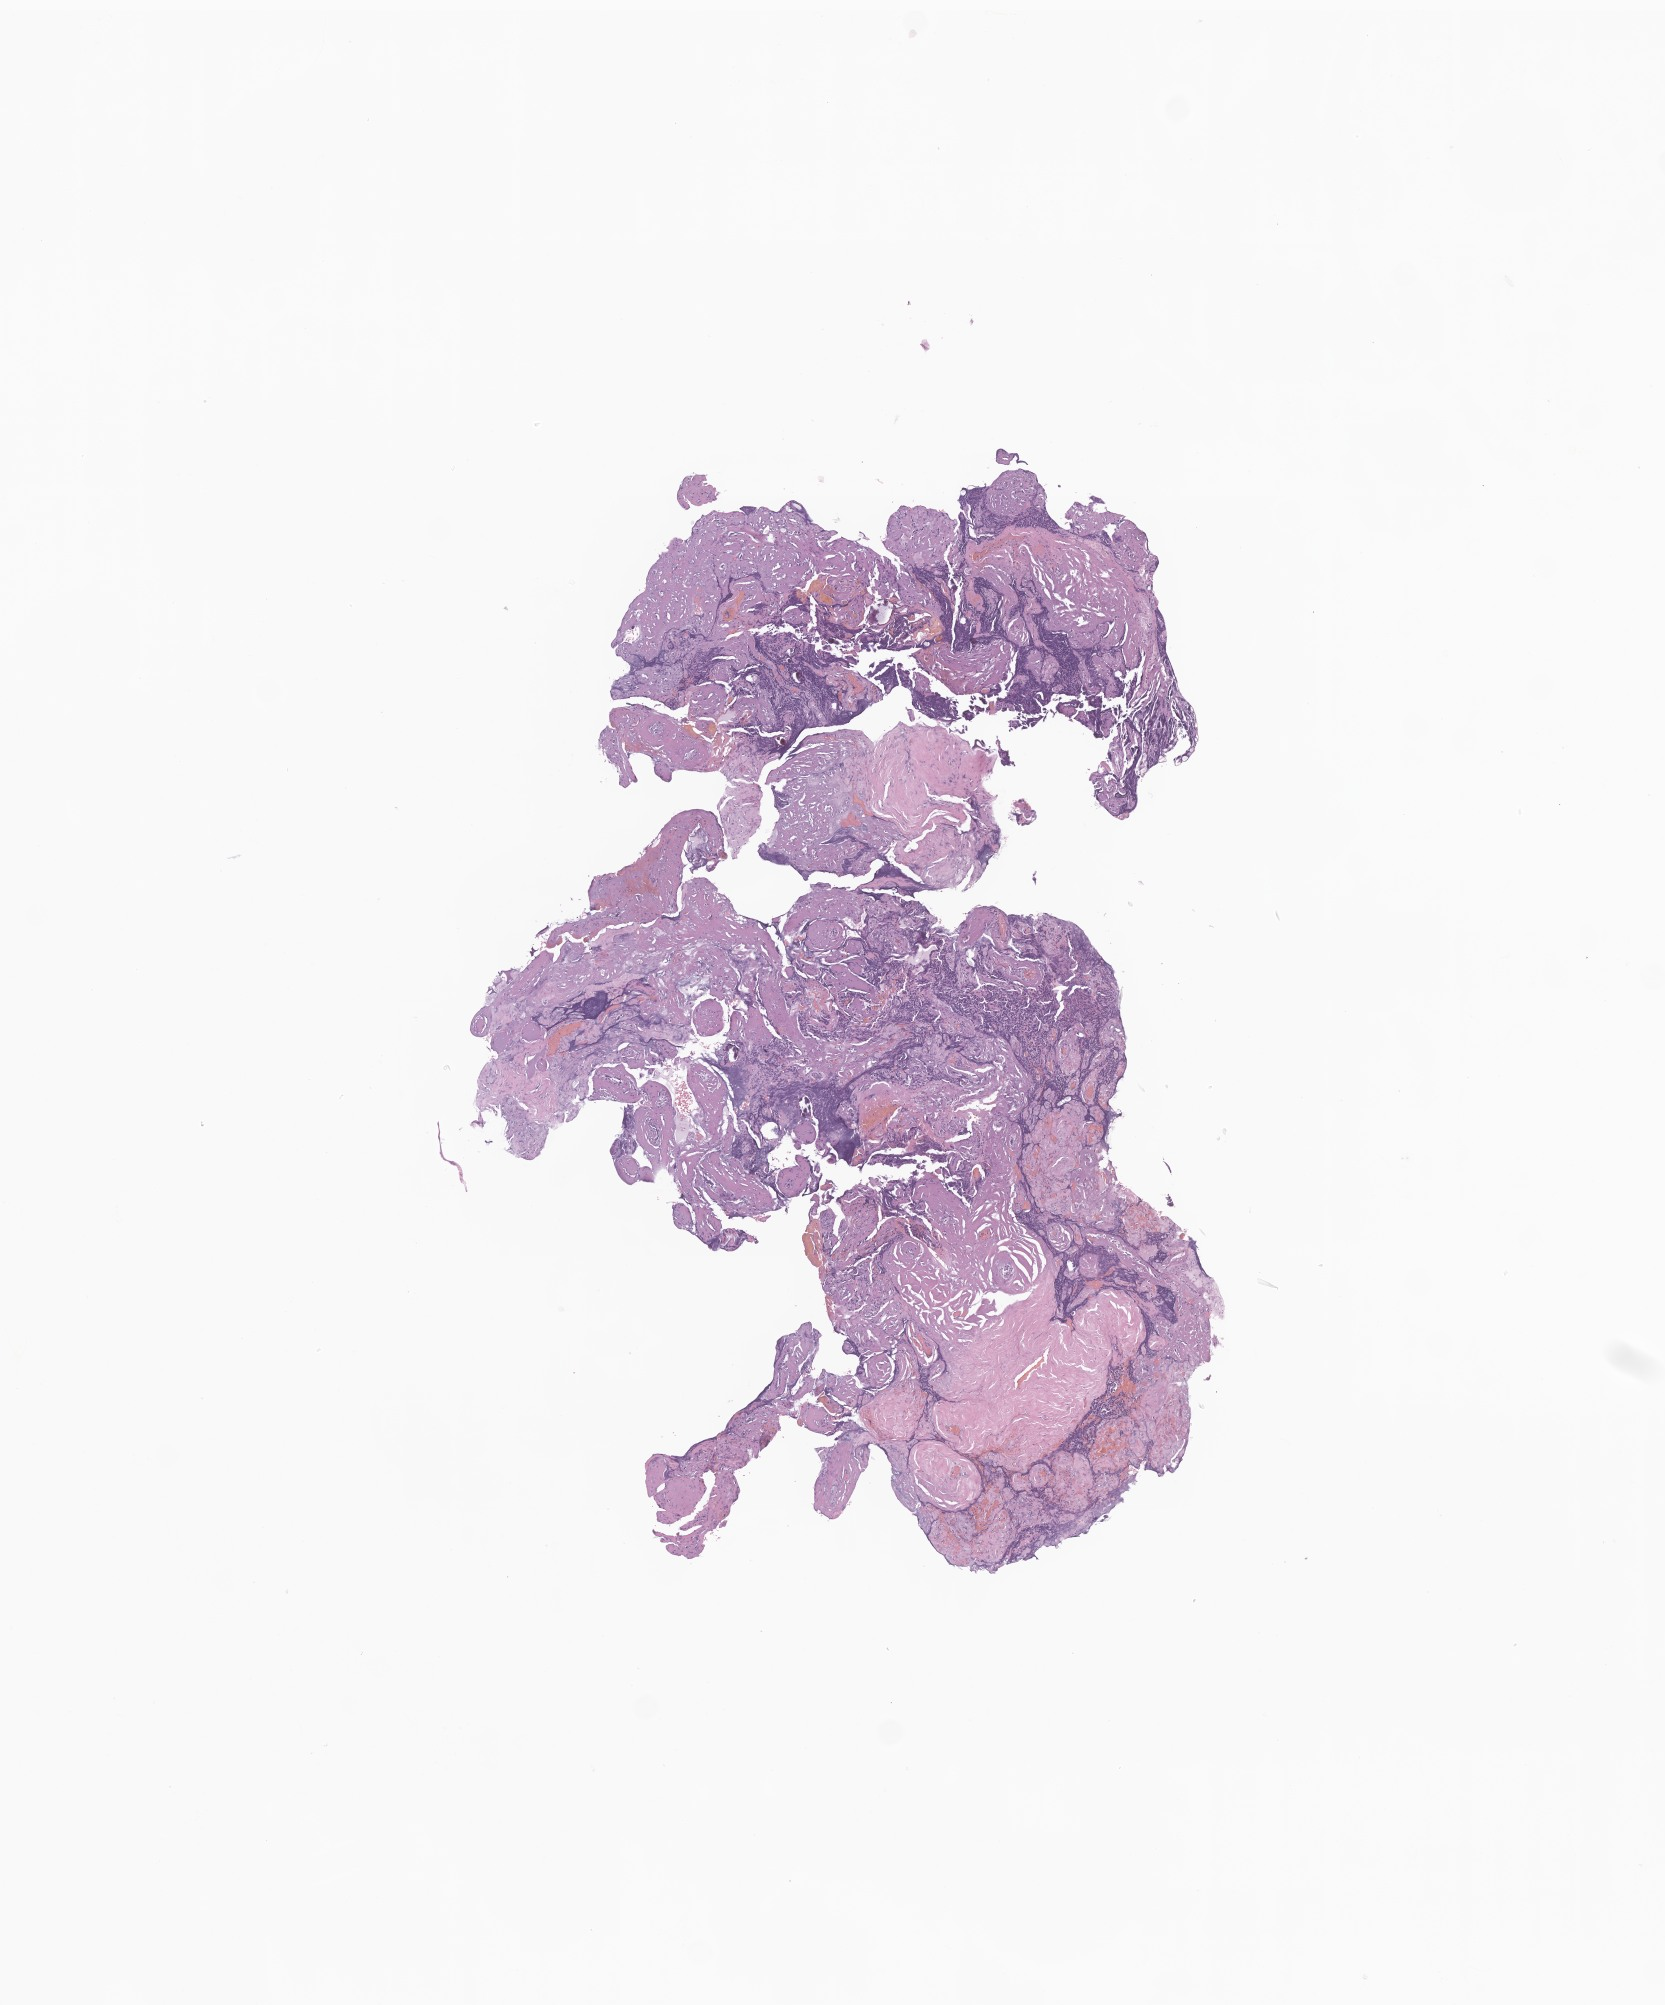
Digitized haematoxylin and eosin-stained section of tumor tissue from the brain — low-resolution overview of the scanned area, about 7.0 x 8.5 mm. Formalin-fixed, paraffin-embedded (FFPE) tissue. Patient: female, age 208 months (17 years 4 months).
Diagnosis: Ependymoma, NOS.